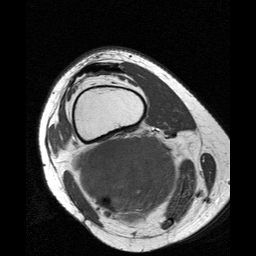
MRI of an extremity soft-tissue mass, one axial slice; slice 20 of 25 in the series (ordered by position); 256 × 256 image matrix, field of view 160 × 160 mm. Female patient. Case-level facts recorded for this patient, not image findings: histological type: liposarcoma; site of the primary tumour: right thigh.
Structures marked on this image (expert manual segmentation):
- gross tumour volume (mass): bounding box (x1, y1, x2, y2) in pixels: (70, 134, 181, 227)